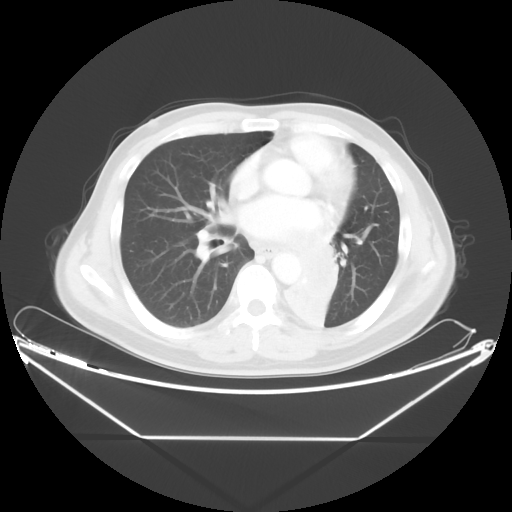
Chest CT, one axial slice; position 22 of 48 along the scan axis; reconstruction kernel STANDARD; 120 kVp; lung window (W 1500 / L -600 HU); 5 mm slice thickness; 512 × 512 image matrix, field of view 438 × 438 mm. Male patient, age 58 years. From the clinical record (not read from this slice): clinical TNM (as recorded): T3 N3 M0.
Structures marked on this image (rectangle marked by the reading radiologist):
- lung tumour (recorded histology: squamous cell carcinoma): box from (x=277, y=233) to (x=348, y=330) px